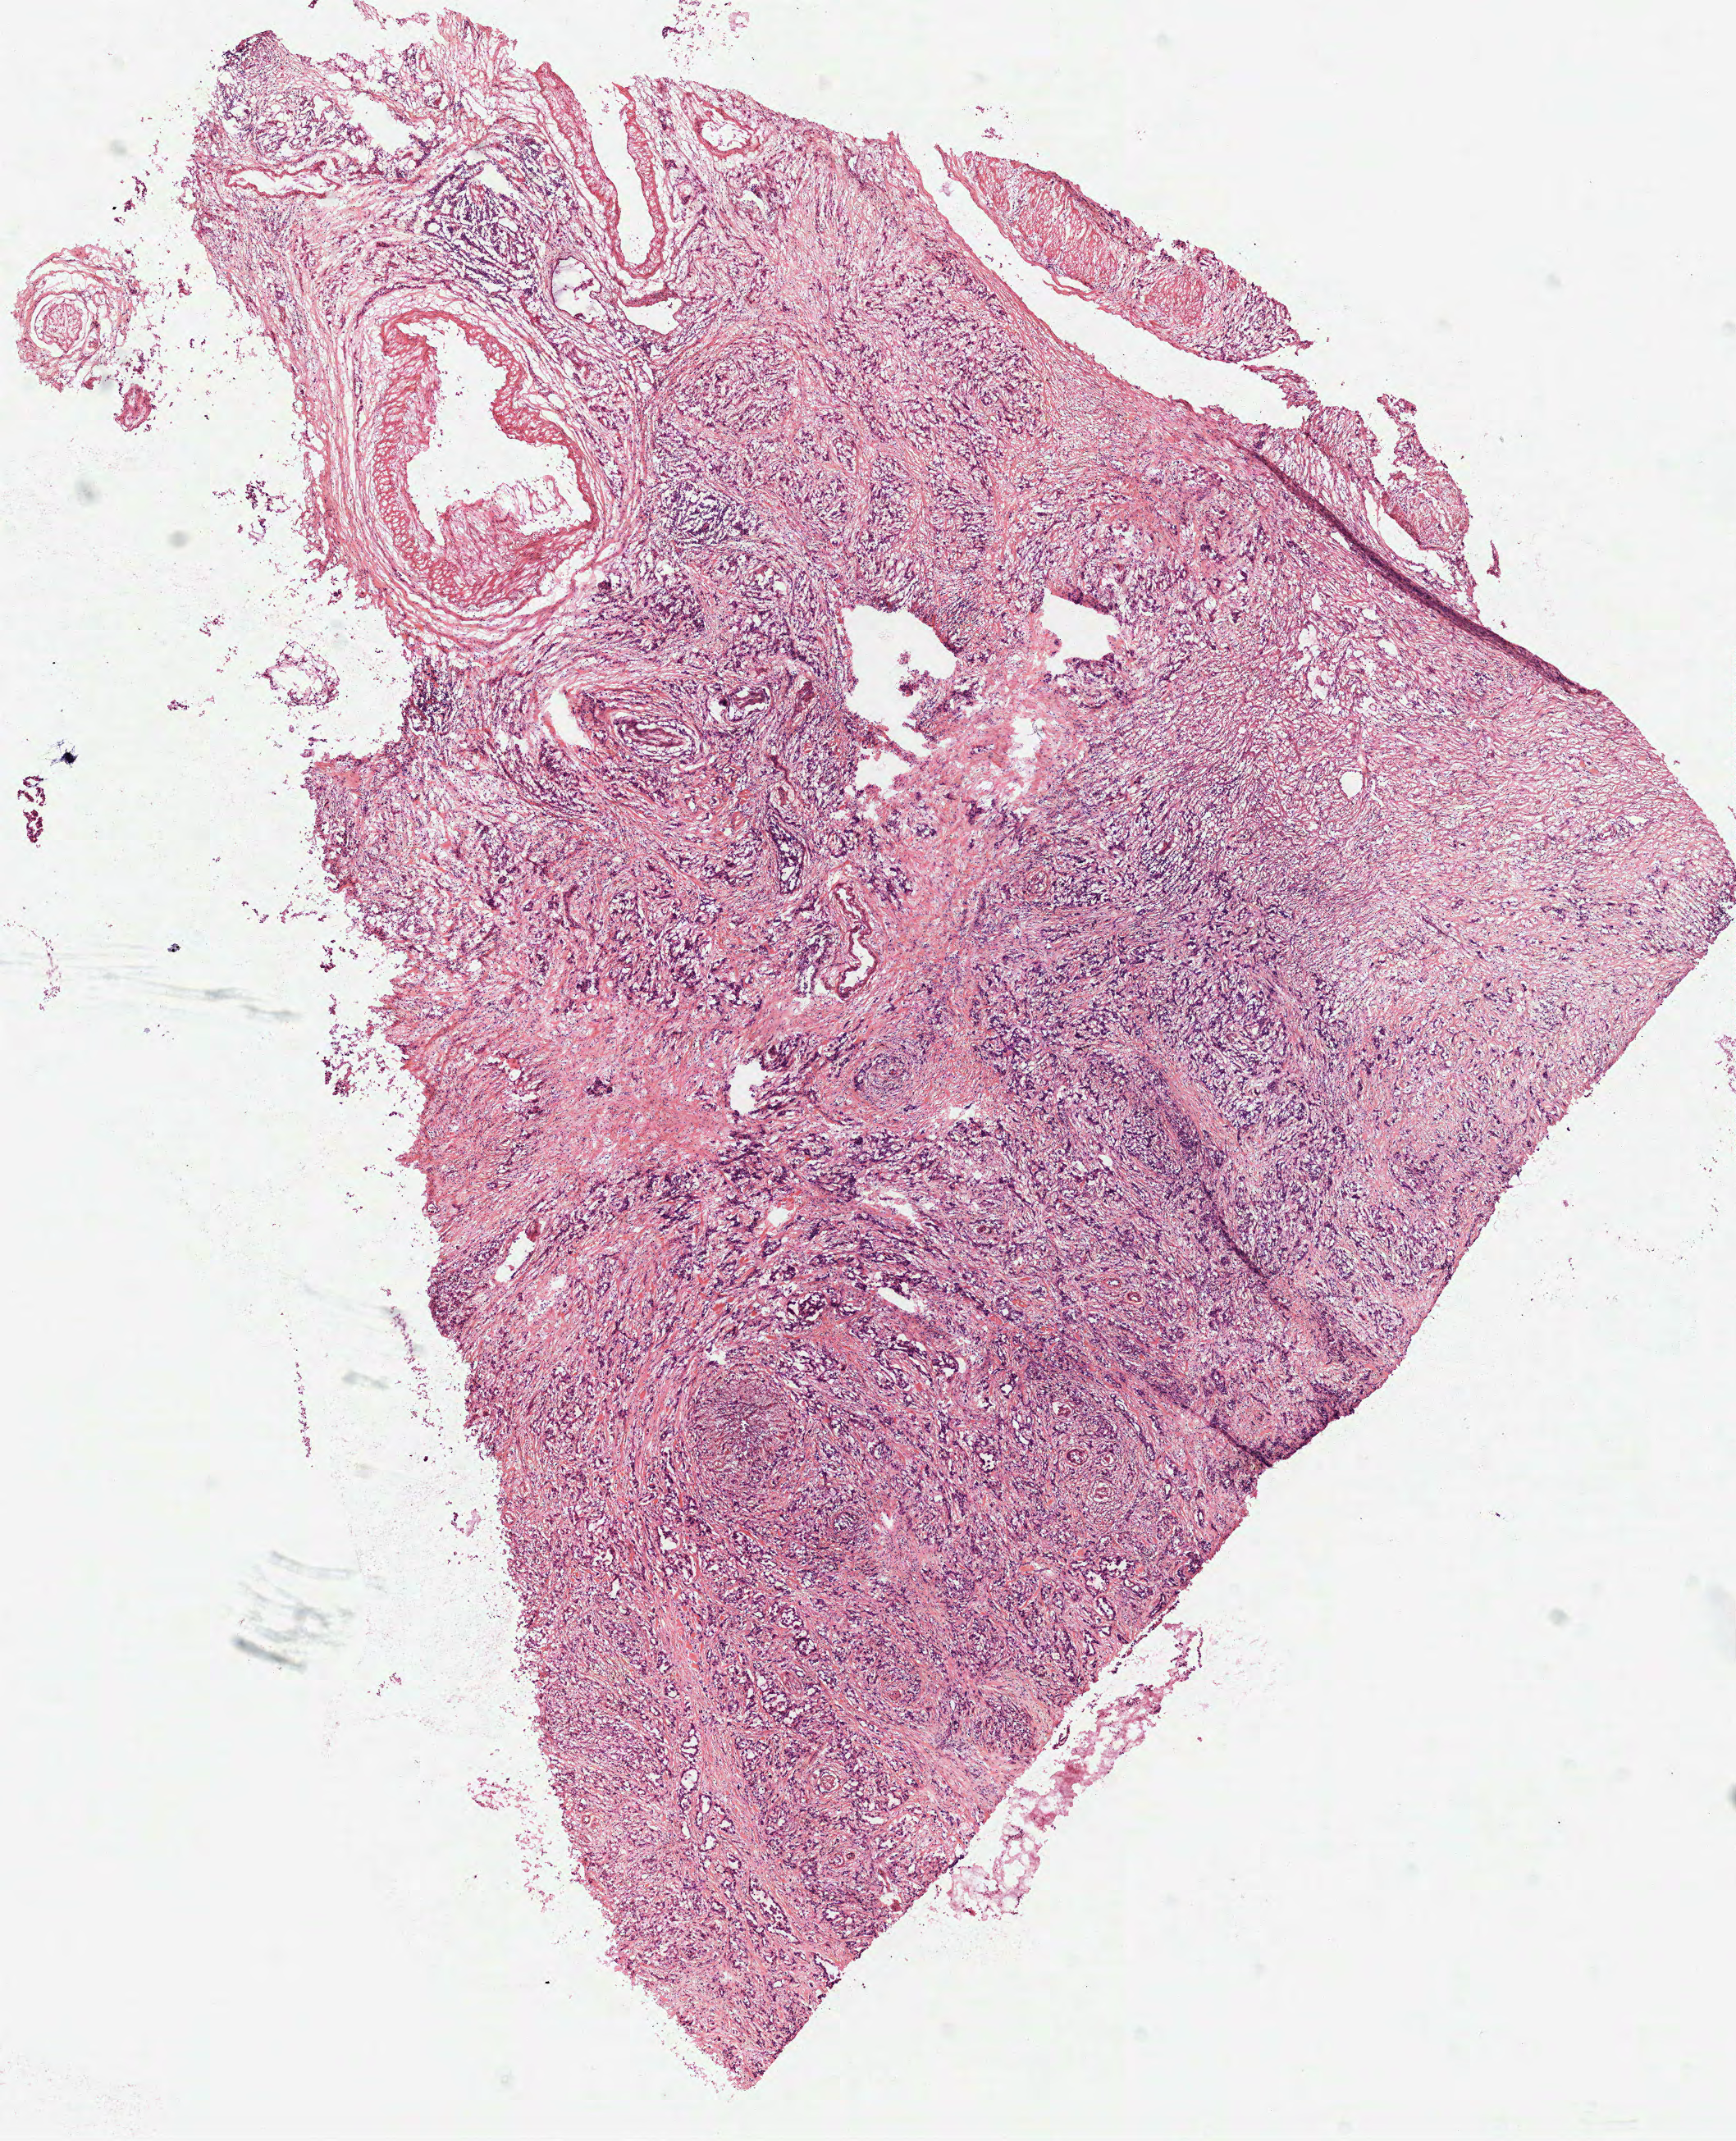
Digitized Hematoxylin and eosin (H&E) stained tissue section (whole slide), low-resolution overview of the scanned area, about 8.5 x 10.5 mm (from a 40x scan), frozen section from the top of the tissue portion, stomach, primary tumour sample. Female patient; age at initial diagnosis 61 years. Histologic grade: G3 (poorly differentiated). Composition of this section per pathologist review: tumour cells 85%, tumour nuclei 80%, normal cells 0%, stromal cells 15%, necrosis 0%.
Diagnosis: Adenocarcinoma, intestinal type (gastric antrum). AJCC pathologic stage: II.